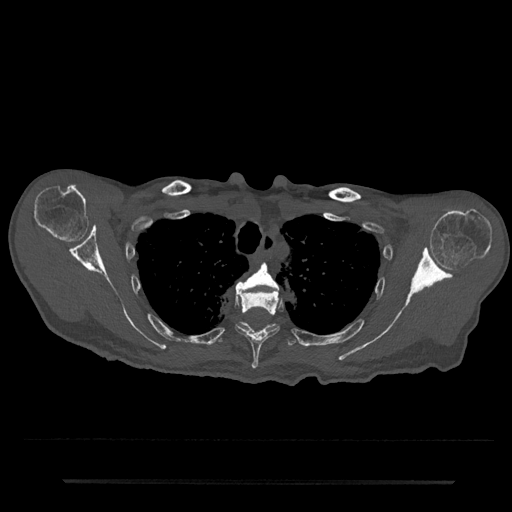
CT including the spine, one axial slice. Slice 619 of 797 in the series (ordered by position). 120 kVp. Bone window (W 1800 / L 400 HU). 0.5 mm slice thickness. 512 × 512 image matrix, field of view 427 × 427 mm. Male patient, age 74 years. Case-level facts recorded for this patient, not image findings: primary cancer: prostate.
Annotated regions visible in this slice (semi-automatic segmentation, software-assisted and operator-edited):
- T3 vertebra: bounding box [x1, y1, x2, y2] px = [236, 263, 279, 293]
- T4 vertebra: [235, 289, 282, 369]
- T5 vertebra: [218, 322, 296, 346]